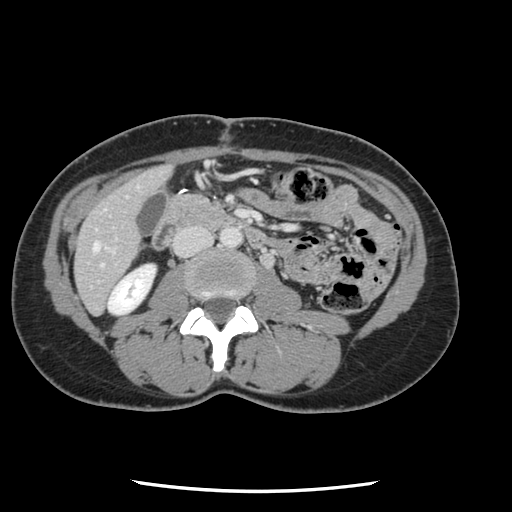
Contrast-enhanced abdominal CT, one axial slice. Slice 24 of 134 in the series (ordered by position). Intravenous contrast given. Soft-tissue window (W 400 / L 40 HU). 512 × 512 image matrix, field of view 330 × 330 mm. Female patient, age 43 years. From the clinical record (not read from this slice): diagnosis: colorectal cancer liver metastases, imaged before liver resection; multiple liver metastases: yes; largest metastasis: 3.4 cm.
Structures marked on this image (expert manual segmentation):
- hepatic veins: bounding box (x1, y1, x2, y2) in pixels: (93, 242, 99, 251)
- liver: (76, 167, 171, 313)
- planned liver remnant (the part of the liver to remain after resection): (76, 167, 171, 313)